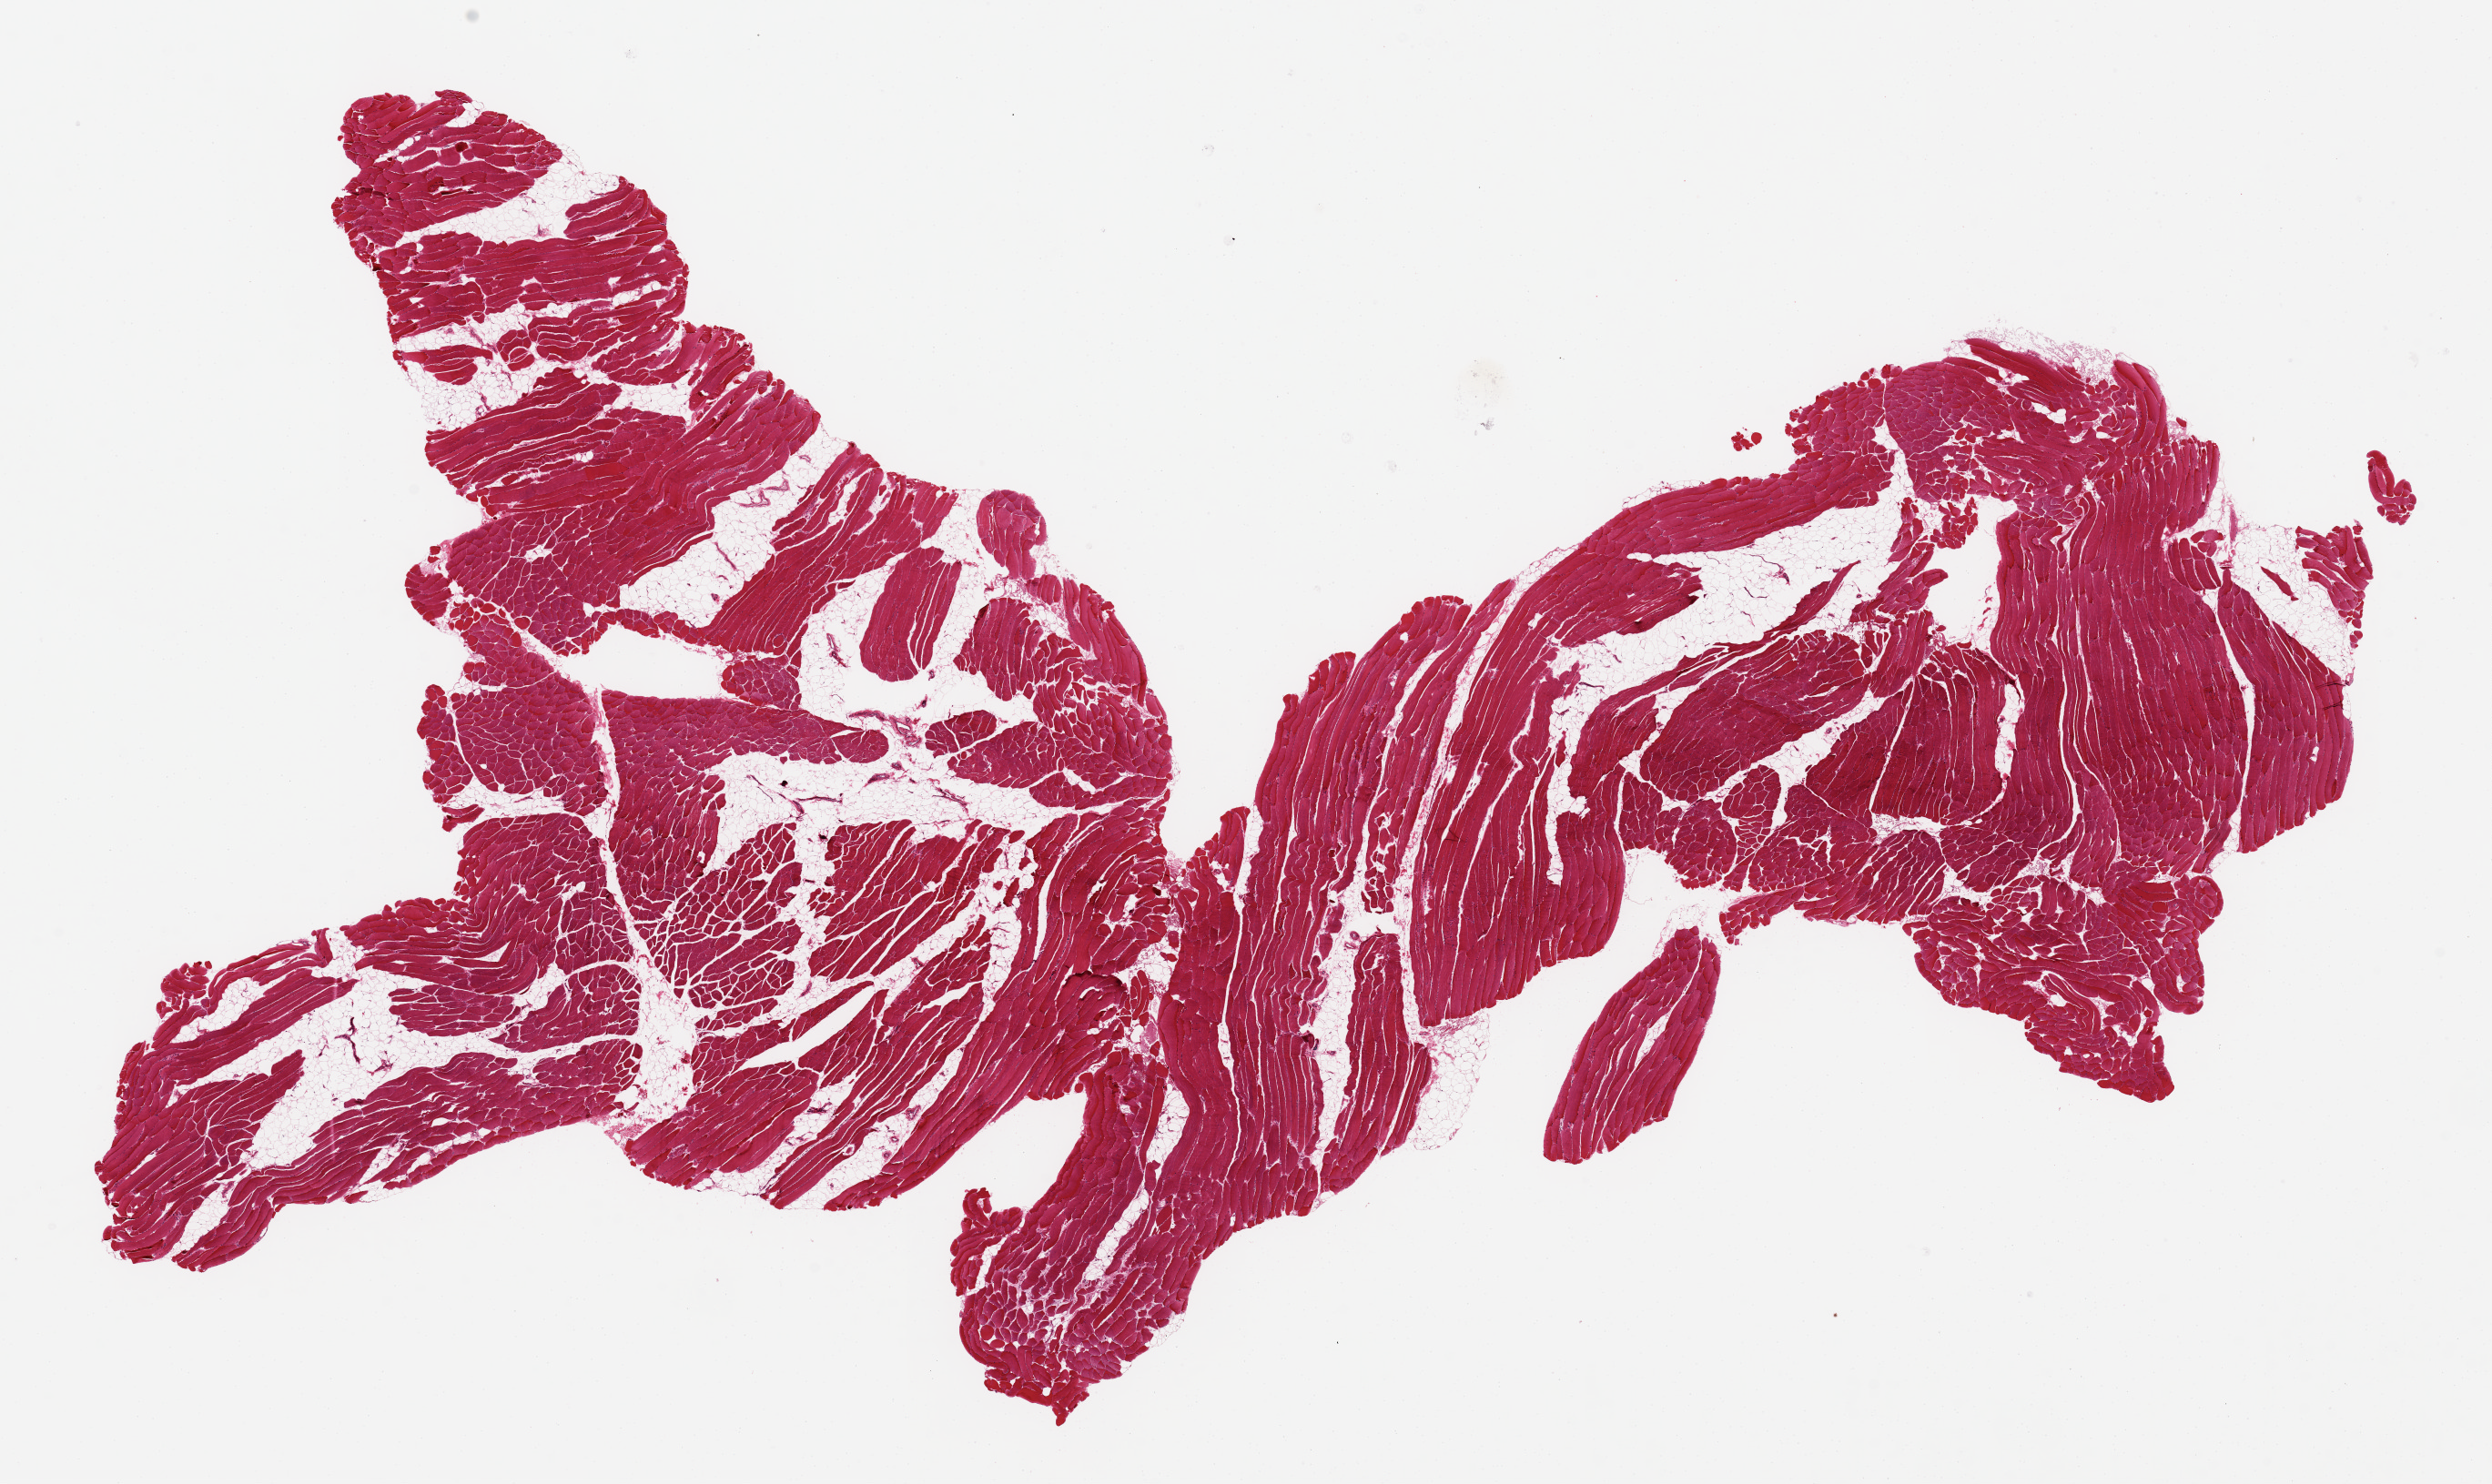
Digitized H&E-stained section, whole scanned area (about 21.7 x 12.9 mm, from a 20x scan) shown as a low-resolution overview; PAXgene-fixed, paraffin-embedded tissue; target tissue: skeletal muscle; donor tissue sample. Male donor.
* pathologist's review note for this sample: 2 aliquots, ~11x7mm. Moderate interstitial fat